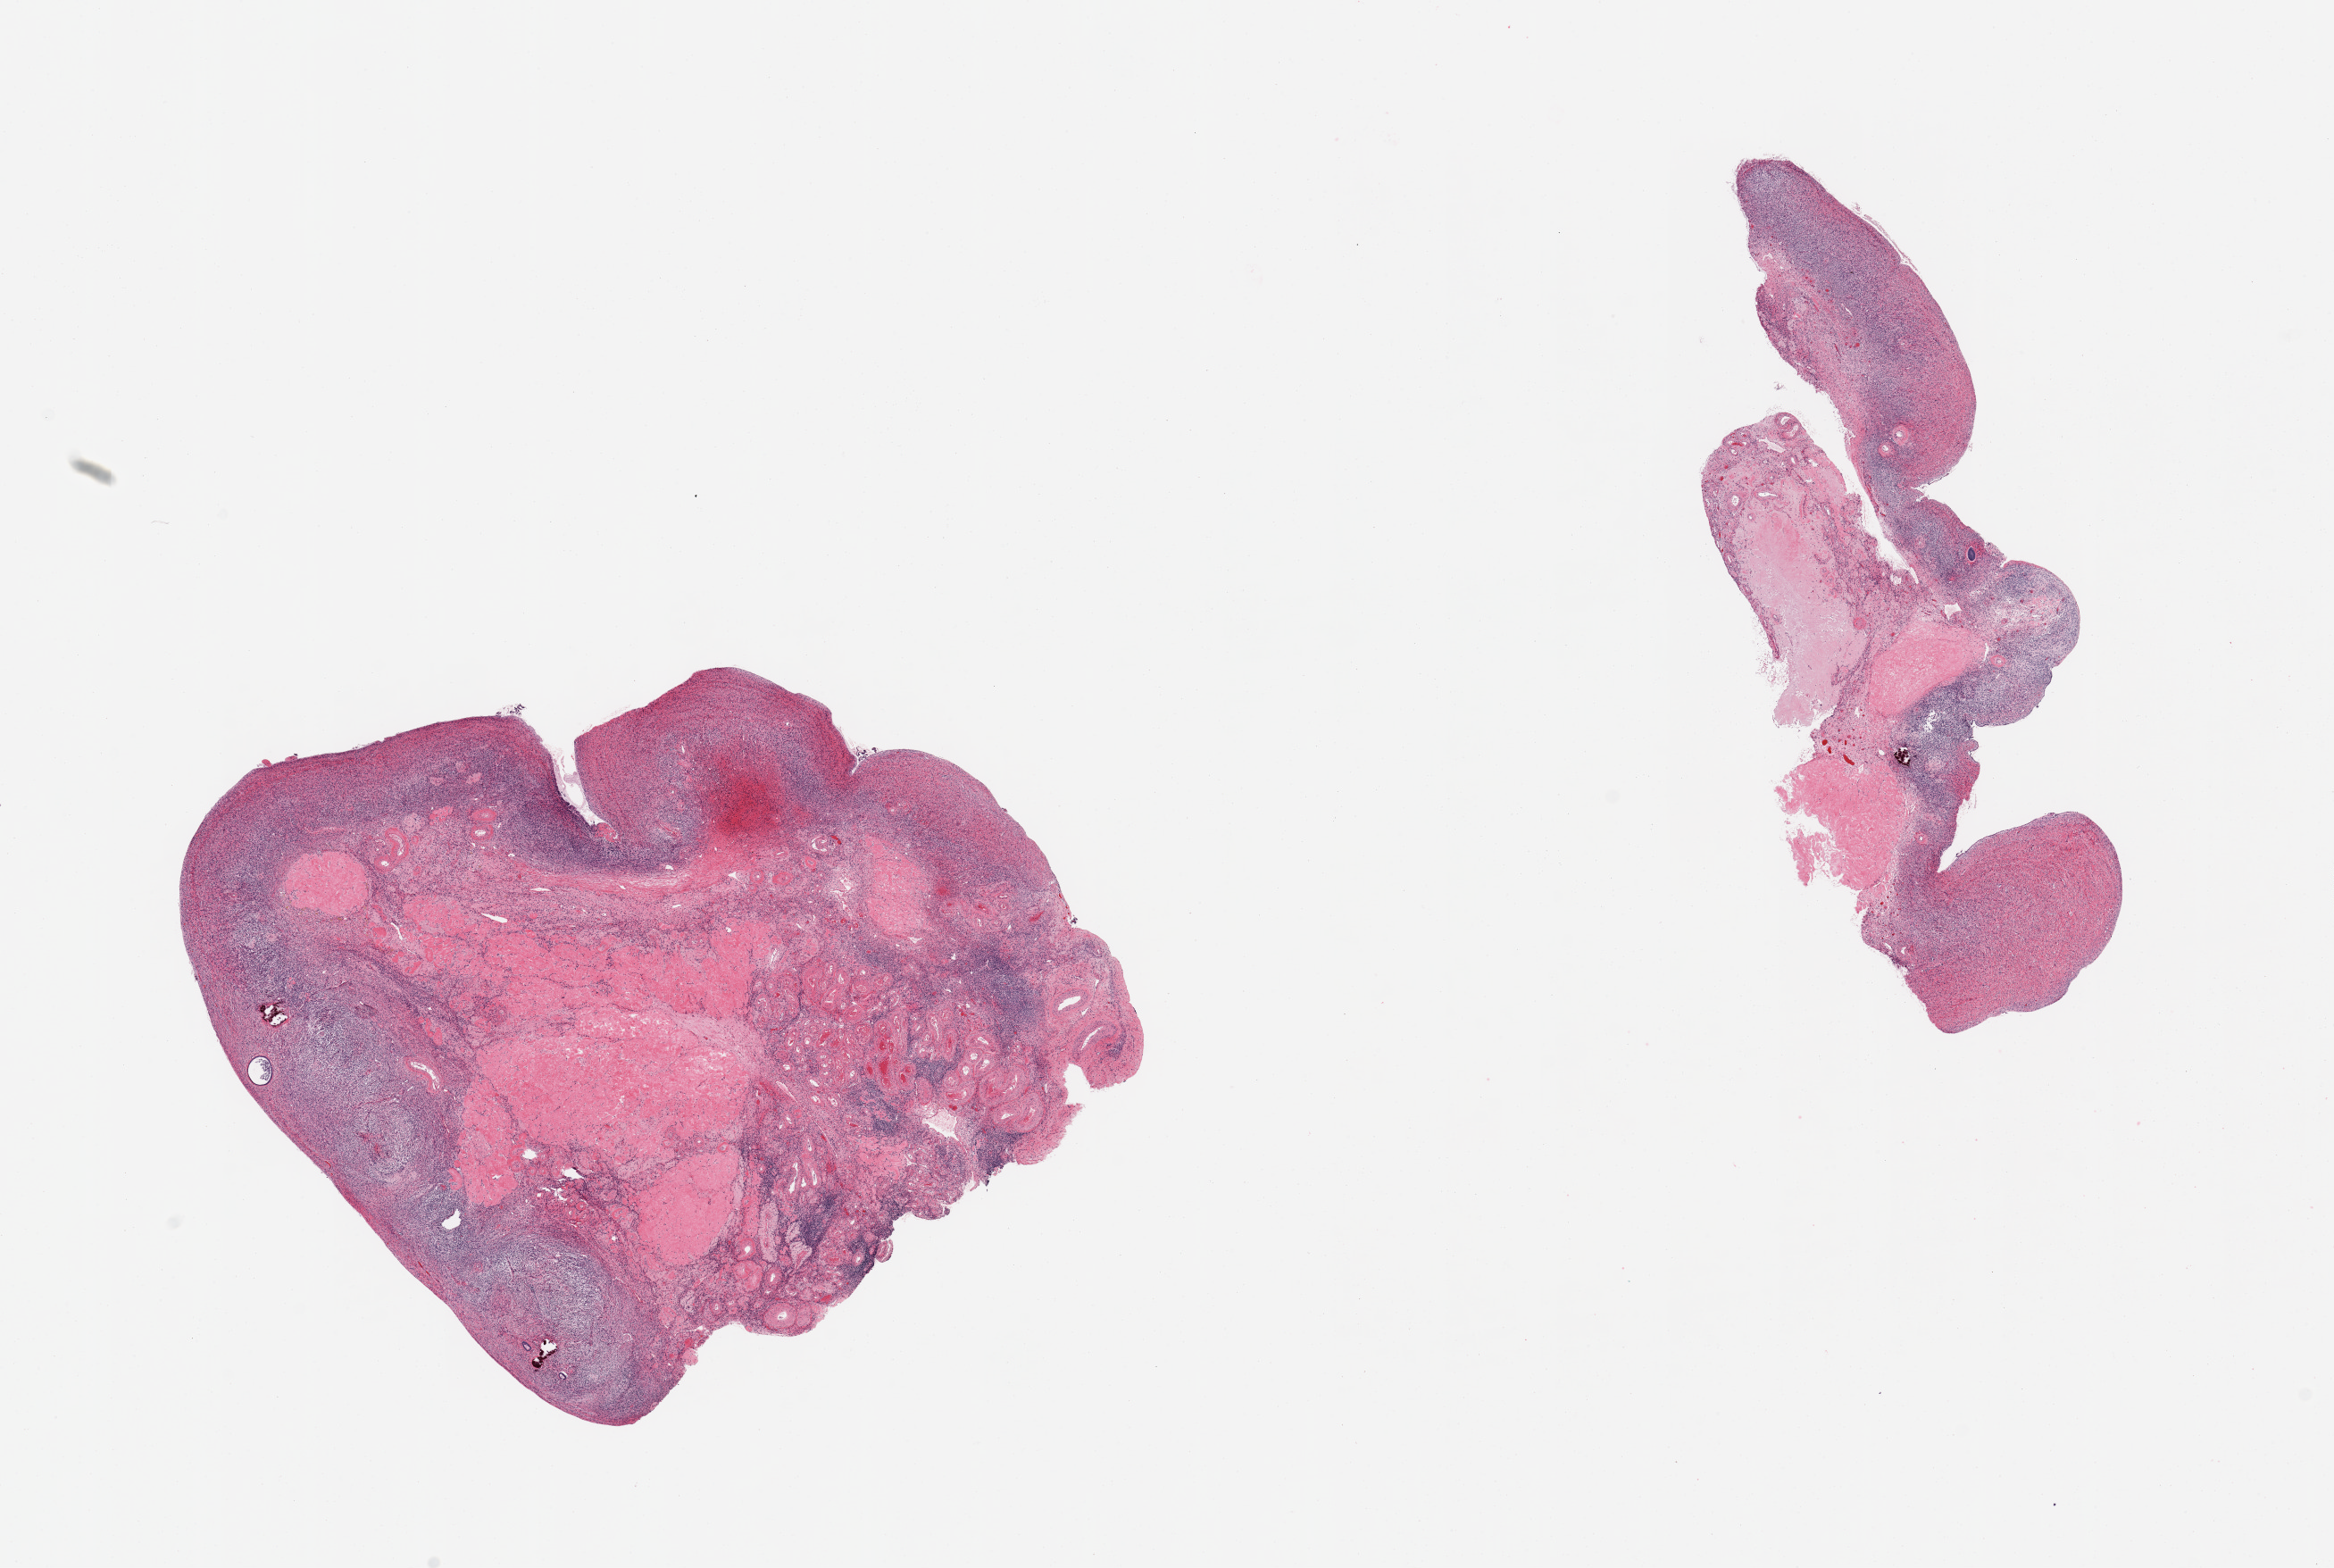
Whole-slide image, H&E stain — shown as a low-resolution overview of the whole scanned area (about 20.7 x 13.9 mm, slide scanned at 20x). PAXgene-fixed paraffin-embedded (PFPE) section. Sampled site (target tissue): ovary. Tissue donor sample.
Pathologist's review note for this sample: 2 pieces.